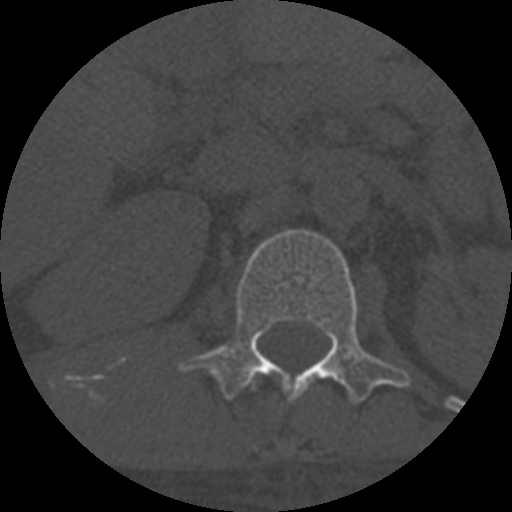
CT including the spine, one axial slice; slice 291 of 708 in the series (ordered by position); reconstruction kernel STANDARD; 120 kVp; one of 3 acquisitions stored at this slice position; bone window (W 1800 / L 400 HU); 1.25 mm slice thickness; 512 × 512 image matrix, field of view 160 × 160 mm. Patient age 55 years. Case-level facts recorded for this patient, not image findings: primary cancer: colon; vertebrae with lytic lesions (as recorded): T12, L1, L5.
Outlined on this slice (semi-automatic segmentation, software-assisted and operator-edited):
- L1 vertebra: bounding box (x1, y1, x2, y2) in pixels: (179, 229, 411, 404)
- T12 vertebra: (248, 379, 255, 387)